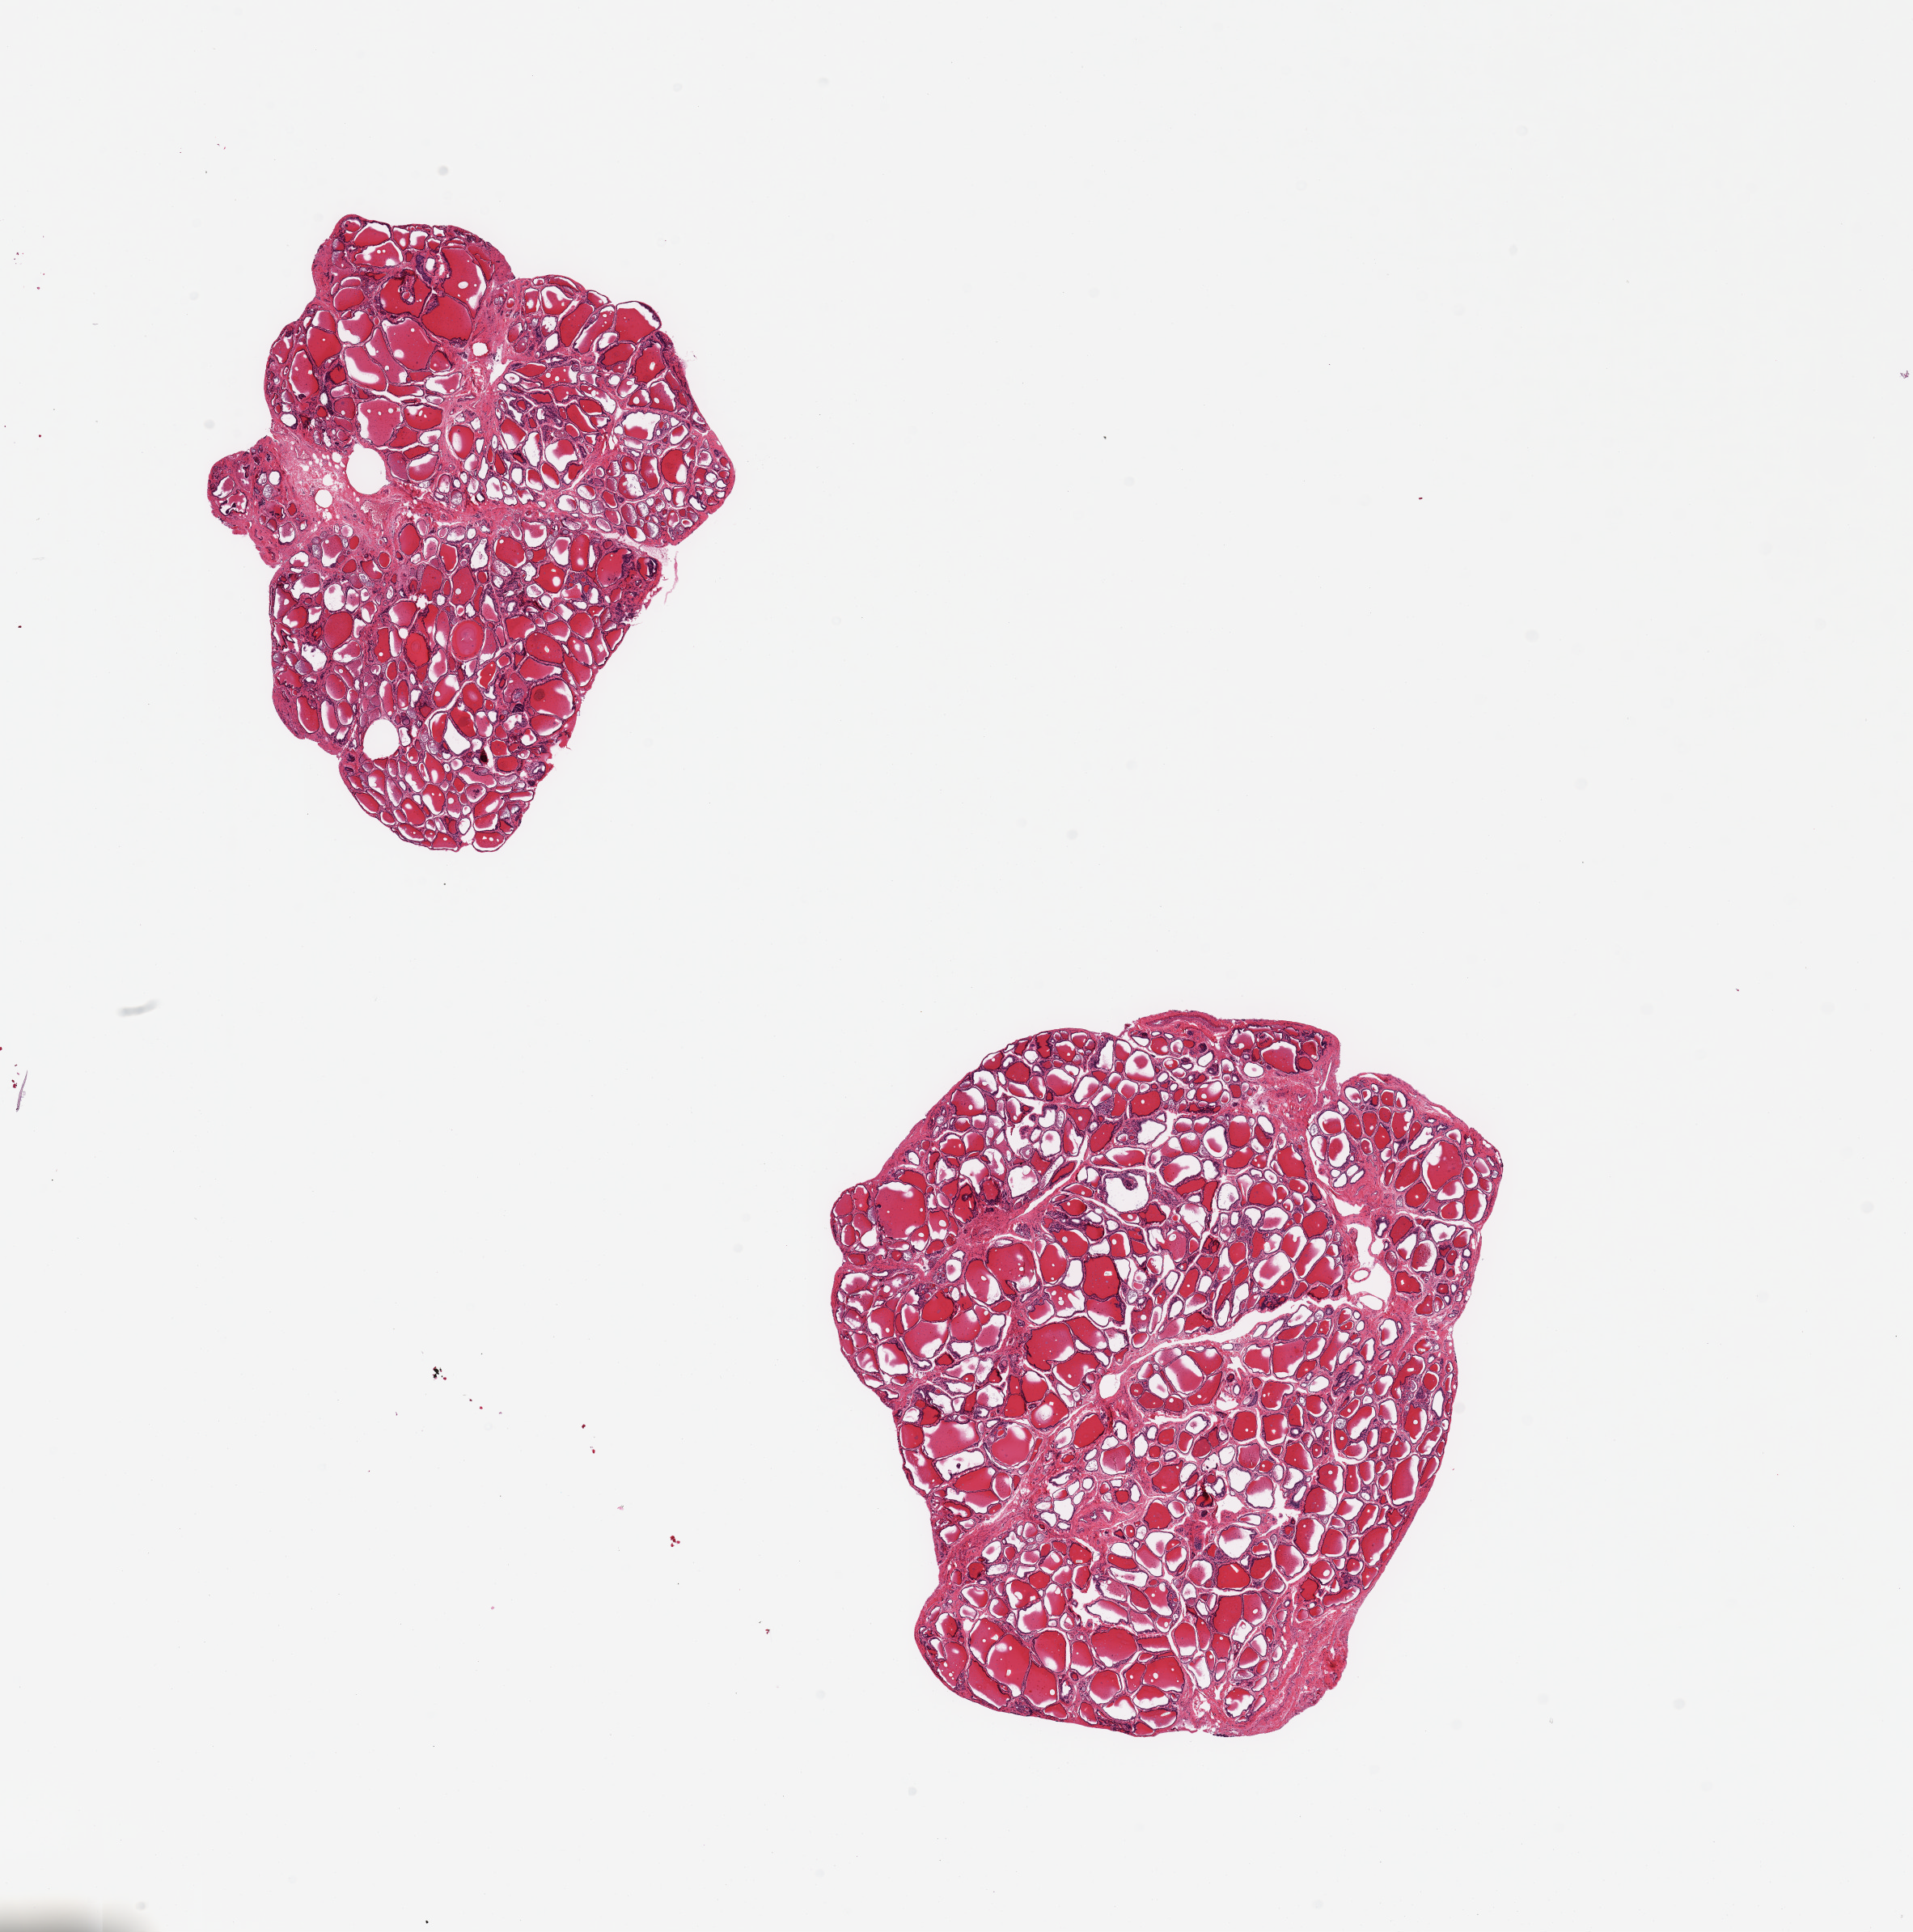
Whole-slide image, hematoxylin and eosin (H&E) stain — whole scanned area (about 18.7 x 18.9 mm) shown as a low-resolution overview, PAXgene-fixed, paraffin-embedded tissue, target tissue: thyroid, tissue donor sample. Donor: male.
• reviewer comment on this tissue sample: 2 pieces; well dissected thyroid with <5% stroma